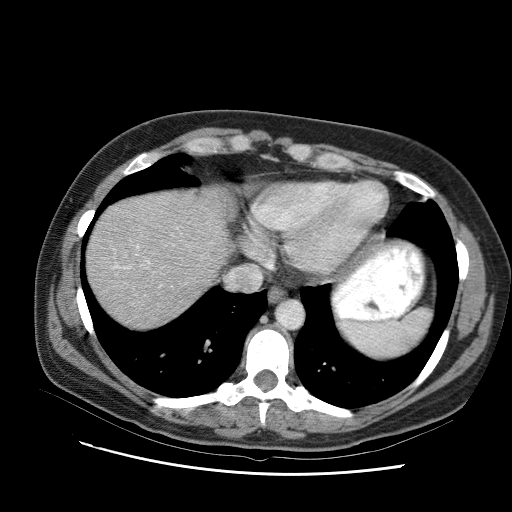
Contrast-enhanced abdominal CT (liver protocol), one axial slice. Position 84 of 95 along the scan axis. Reconstruction kernel STANDARD. 120 kVp. One of 2 acquisitions stored at this slice position. Soft-tissue window (W 400 / L 40 HU). 2.5 mm slice thickness. 512 × 512 image matrix, field of view 360 × 360 mm. From the clinical record (not read from this slice): diagnosis: hepatocellular carcinoma (patient treated with transarterial chemoembolisation; whether this scan precedes or follows treatment is not stated here); TNM stage (as recorded): Stage-I; Child-Pugh class: B; tumour differentiation: moderately differentiated; tumour nodularity: uninodular.
Outlined on this slice (semi-automatic segmentation, software-assisted and operator-edited):
- liver parenchyma outside the tumour (the mass and vessels are separate outlines, so this box may not span the whole liver): bounding box <94,200,210,302> (left, top, right, bottom; pixels)
- liver vessels: <197,211,205,217>